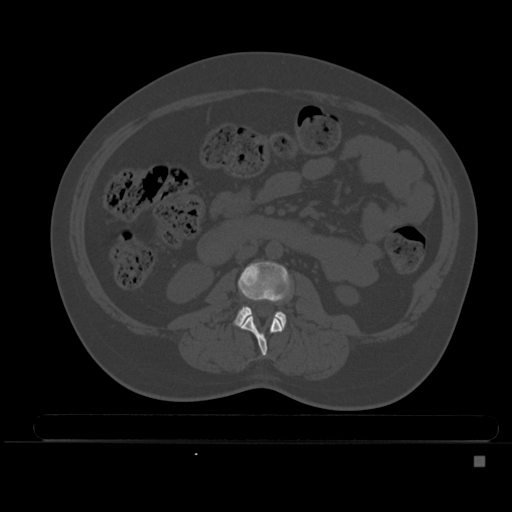
CT including the spine, one axial slice; position 161 of 495 along the scan axis; bone window (W 1800 / L 400 HU); 1.5 mm slice thickness; 512 × 512 image matrix, field of view 404 × 404 mm. Patient: female, 33 years. Case-level facts recorded for this patient, not image findings: primary cancer: breast.
Structures marked on this image (semi-automatically segmented with operator editing):
- L2 vertebra: bounding box [x1, y1, x2, y2] px = [239, 315, 284, 356]
- L3 vertebra: [234, 261, 290, 327]